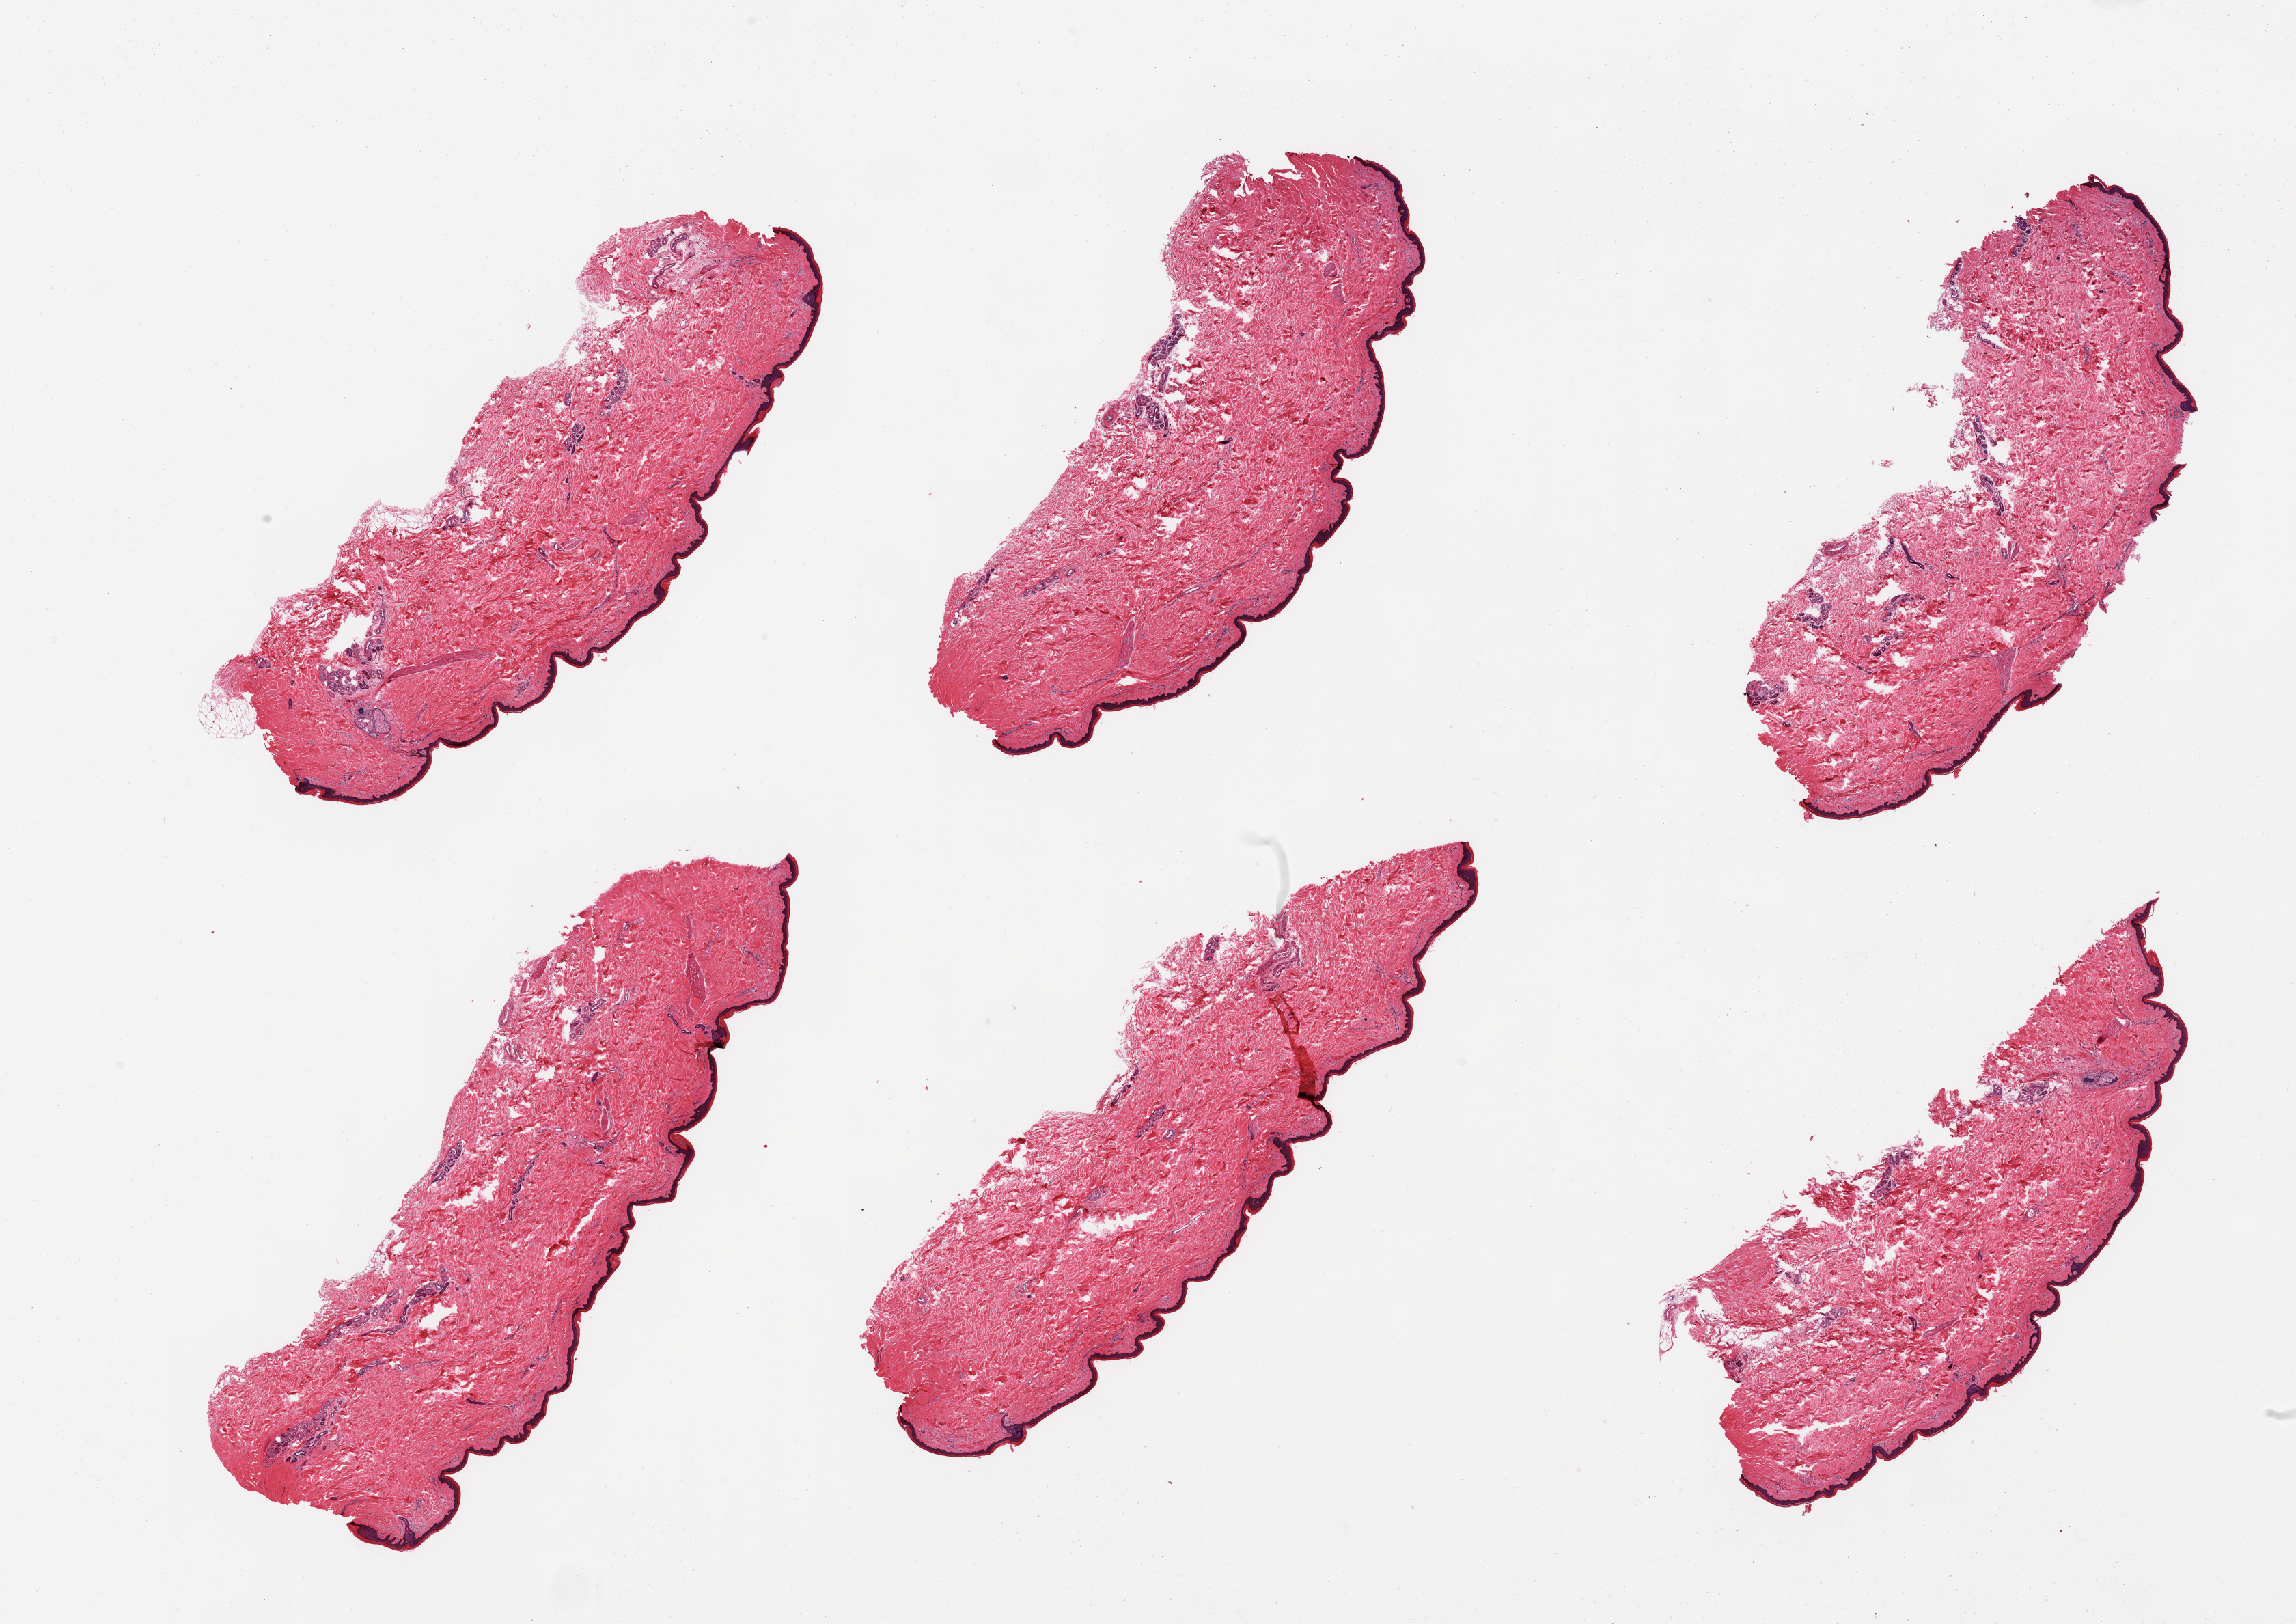
Whole-slide image, H&E stain, low-resolution overview of the scanned area, about 26.6 x 18.8 mm (slide scanned at 20x); PAXgene-fixed paraffin-embedded (PFPE) section; sampled site (target tissue): skin of lower leg; tissue donor sample. Donor sex: male.
Pathologist's review note for this sample: 6 pieces; 1% dermal fat; well trimmed.